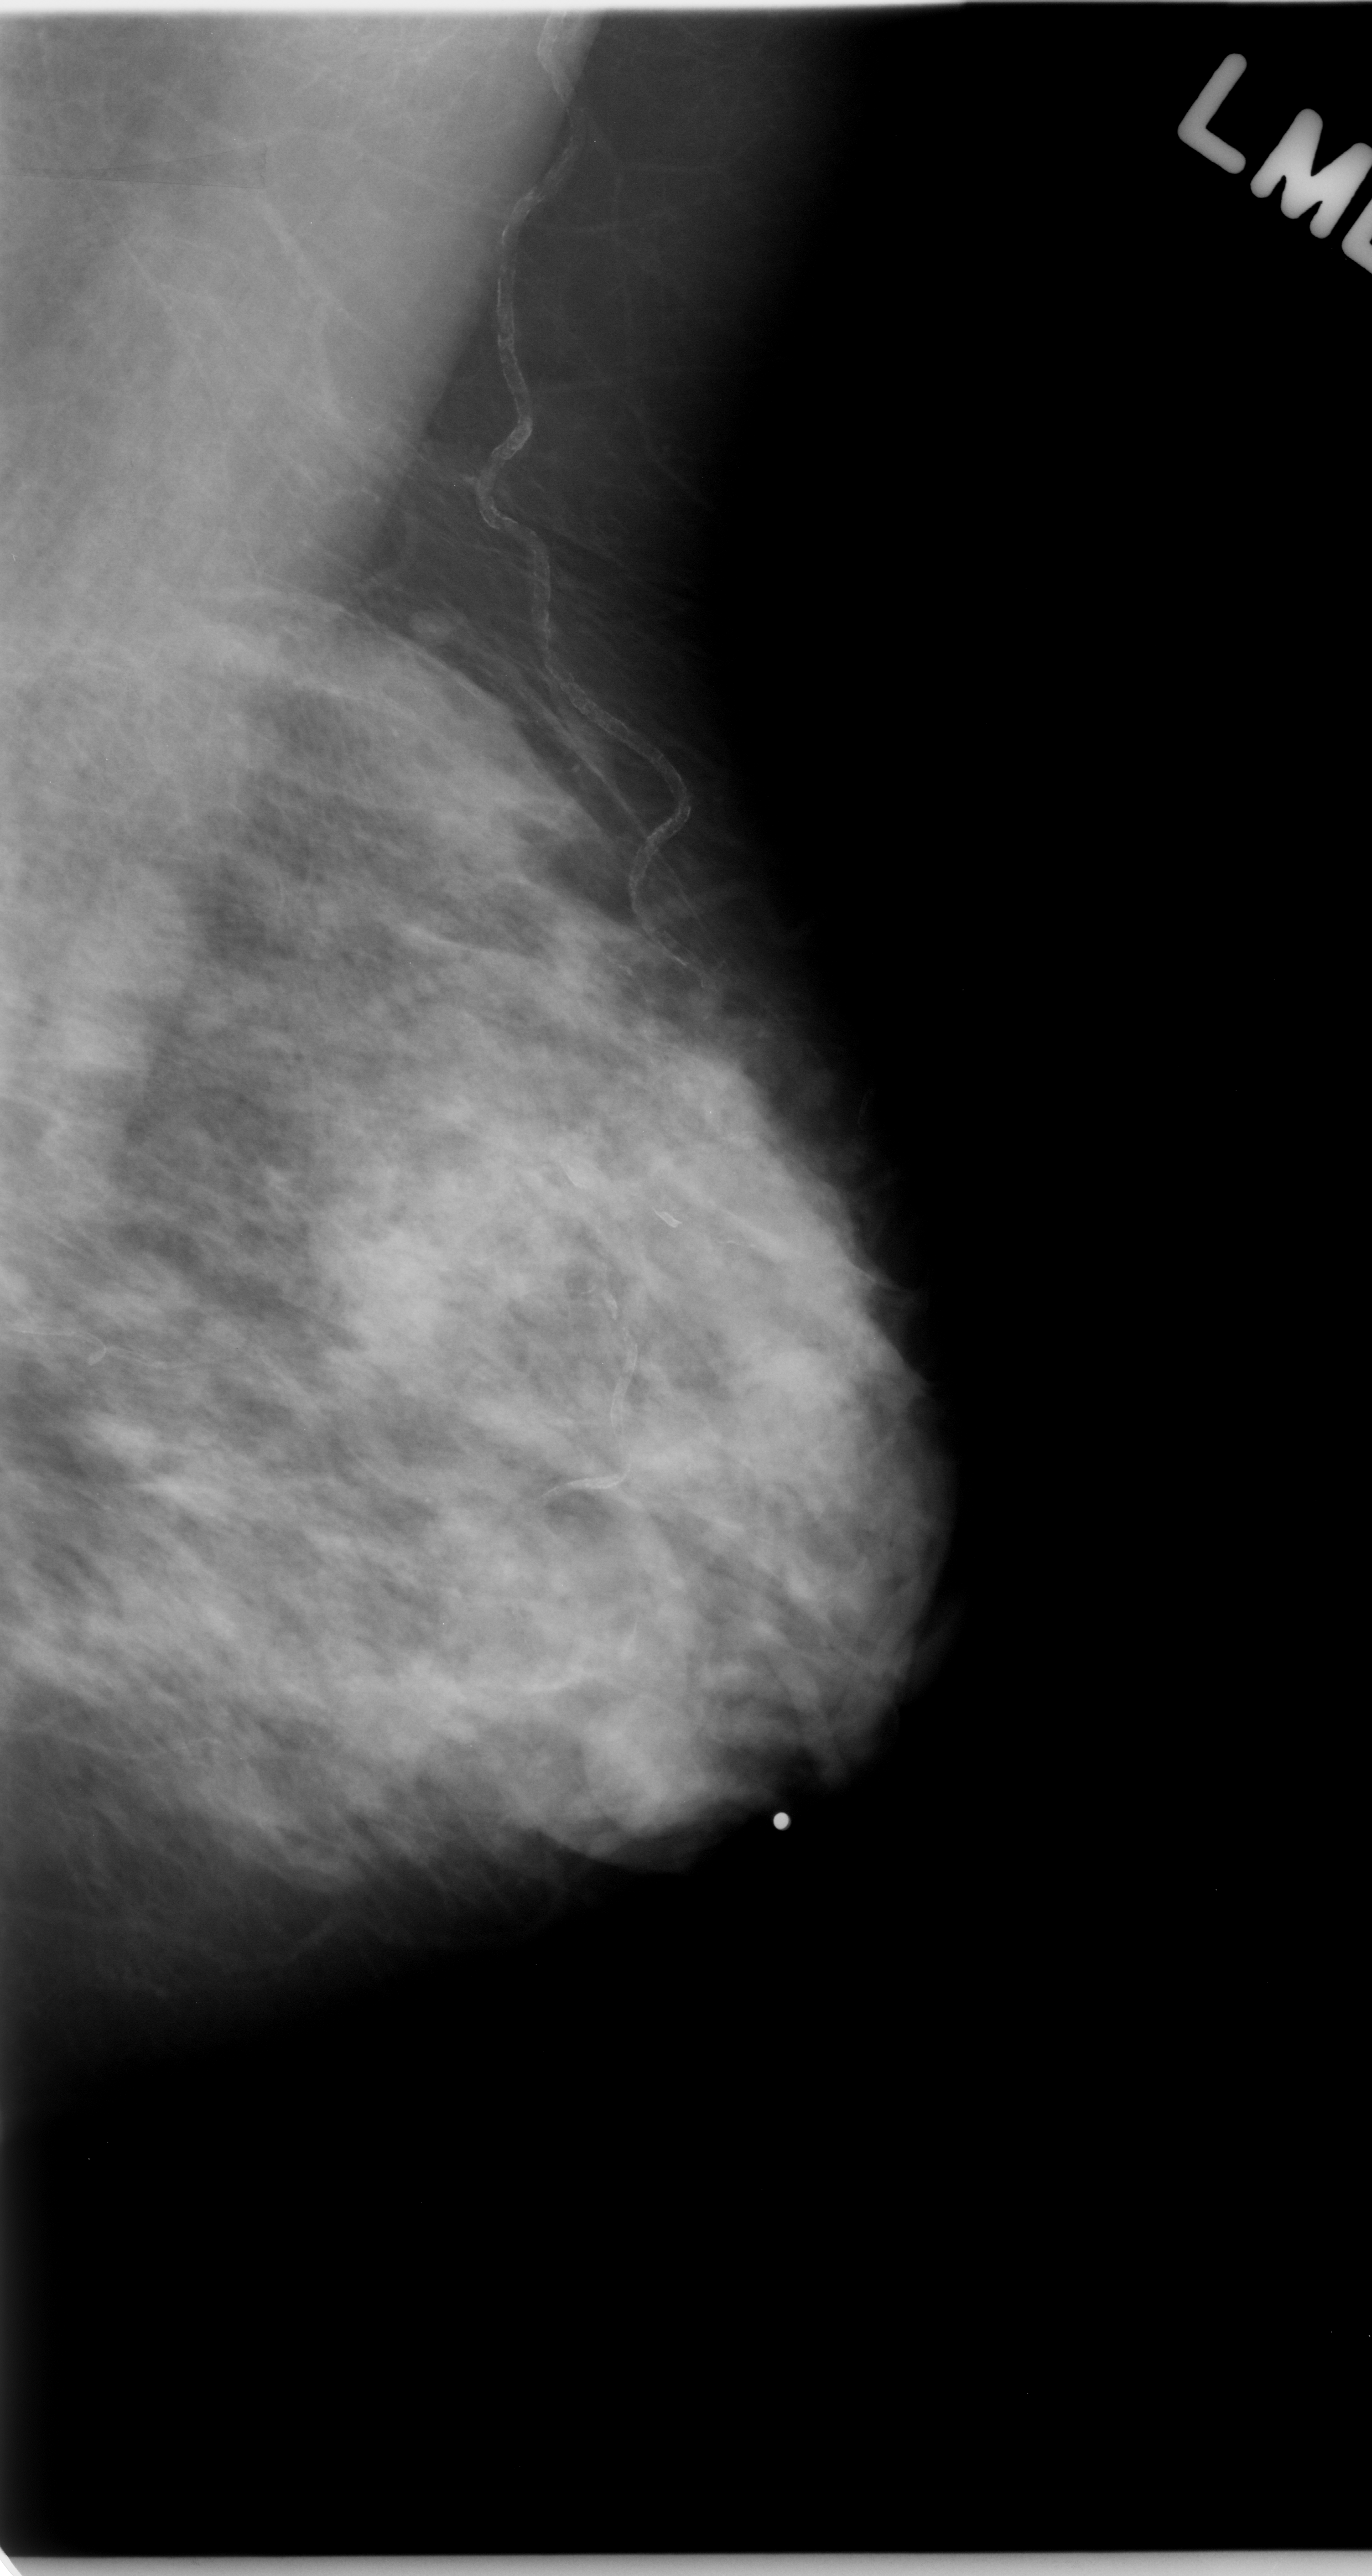
Digitized screen-film mammogram, left breast, mediolateral oblique (MLO) view, breast composition: heterogeneously dense (BI-RADS density category 3 of 4).
Abnormality record for this image: mass, shape oval, margins circumscribed; BI-RADS assessment category 3; pathology (as recorded): benign.